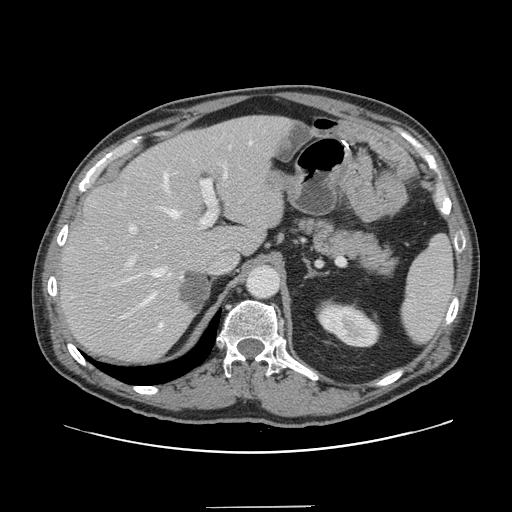
Contrast-enhanced abdominal CT, one axial slice; slice 101 of 139 in the series (ordered by position); 120 kVp; intravenous contrast given; soft-tissue window (W 400 / L 40 HU); 2.5 mm slice thickness; 512 × 512 image matrix, field of view 397 × 397 mm. Male patient, age 64 years. From the clinical record (not read from this slice): diagnosis: colorectal cancer liver metastases, imaged before liver resection; multiple liver metastases: yes; largest metastasis: 3.5 cm.
Annotated regions visible in this slice (expert manual segmentation):
- hepatic veins: bounding box [x1, y1, x2, y2] px = [119, 141, 252, 332]
- liver: [61, 117, 289, 361]
- planned liver remnant (the part of the liver to remain after resection): [60, 117, 276, 361]
- portal vein (with intrahepatic branches): [126, 146, 231, 267]
- liver metastasis: [181, 272, 207, 312]